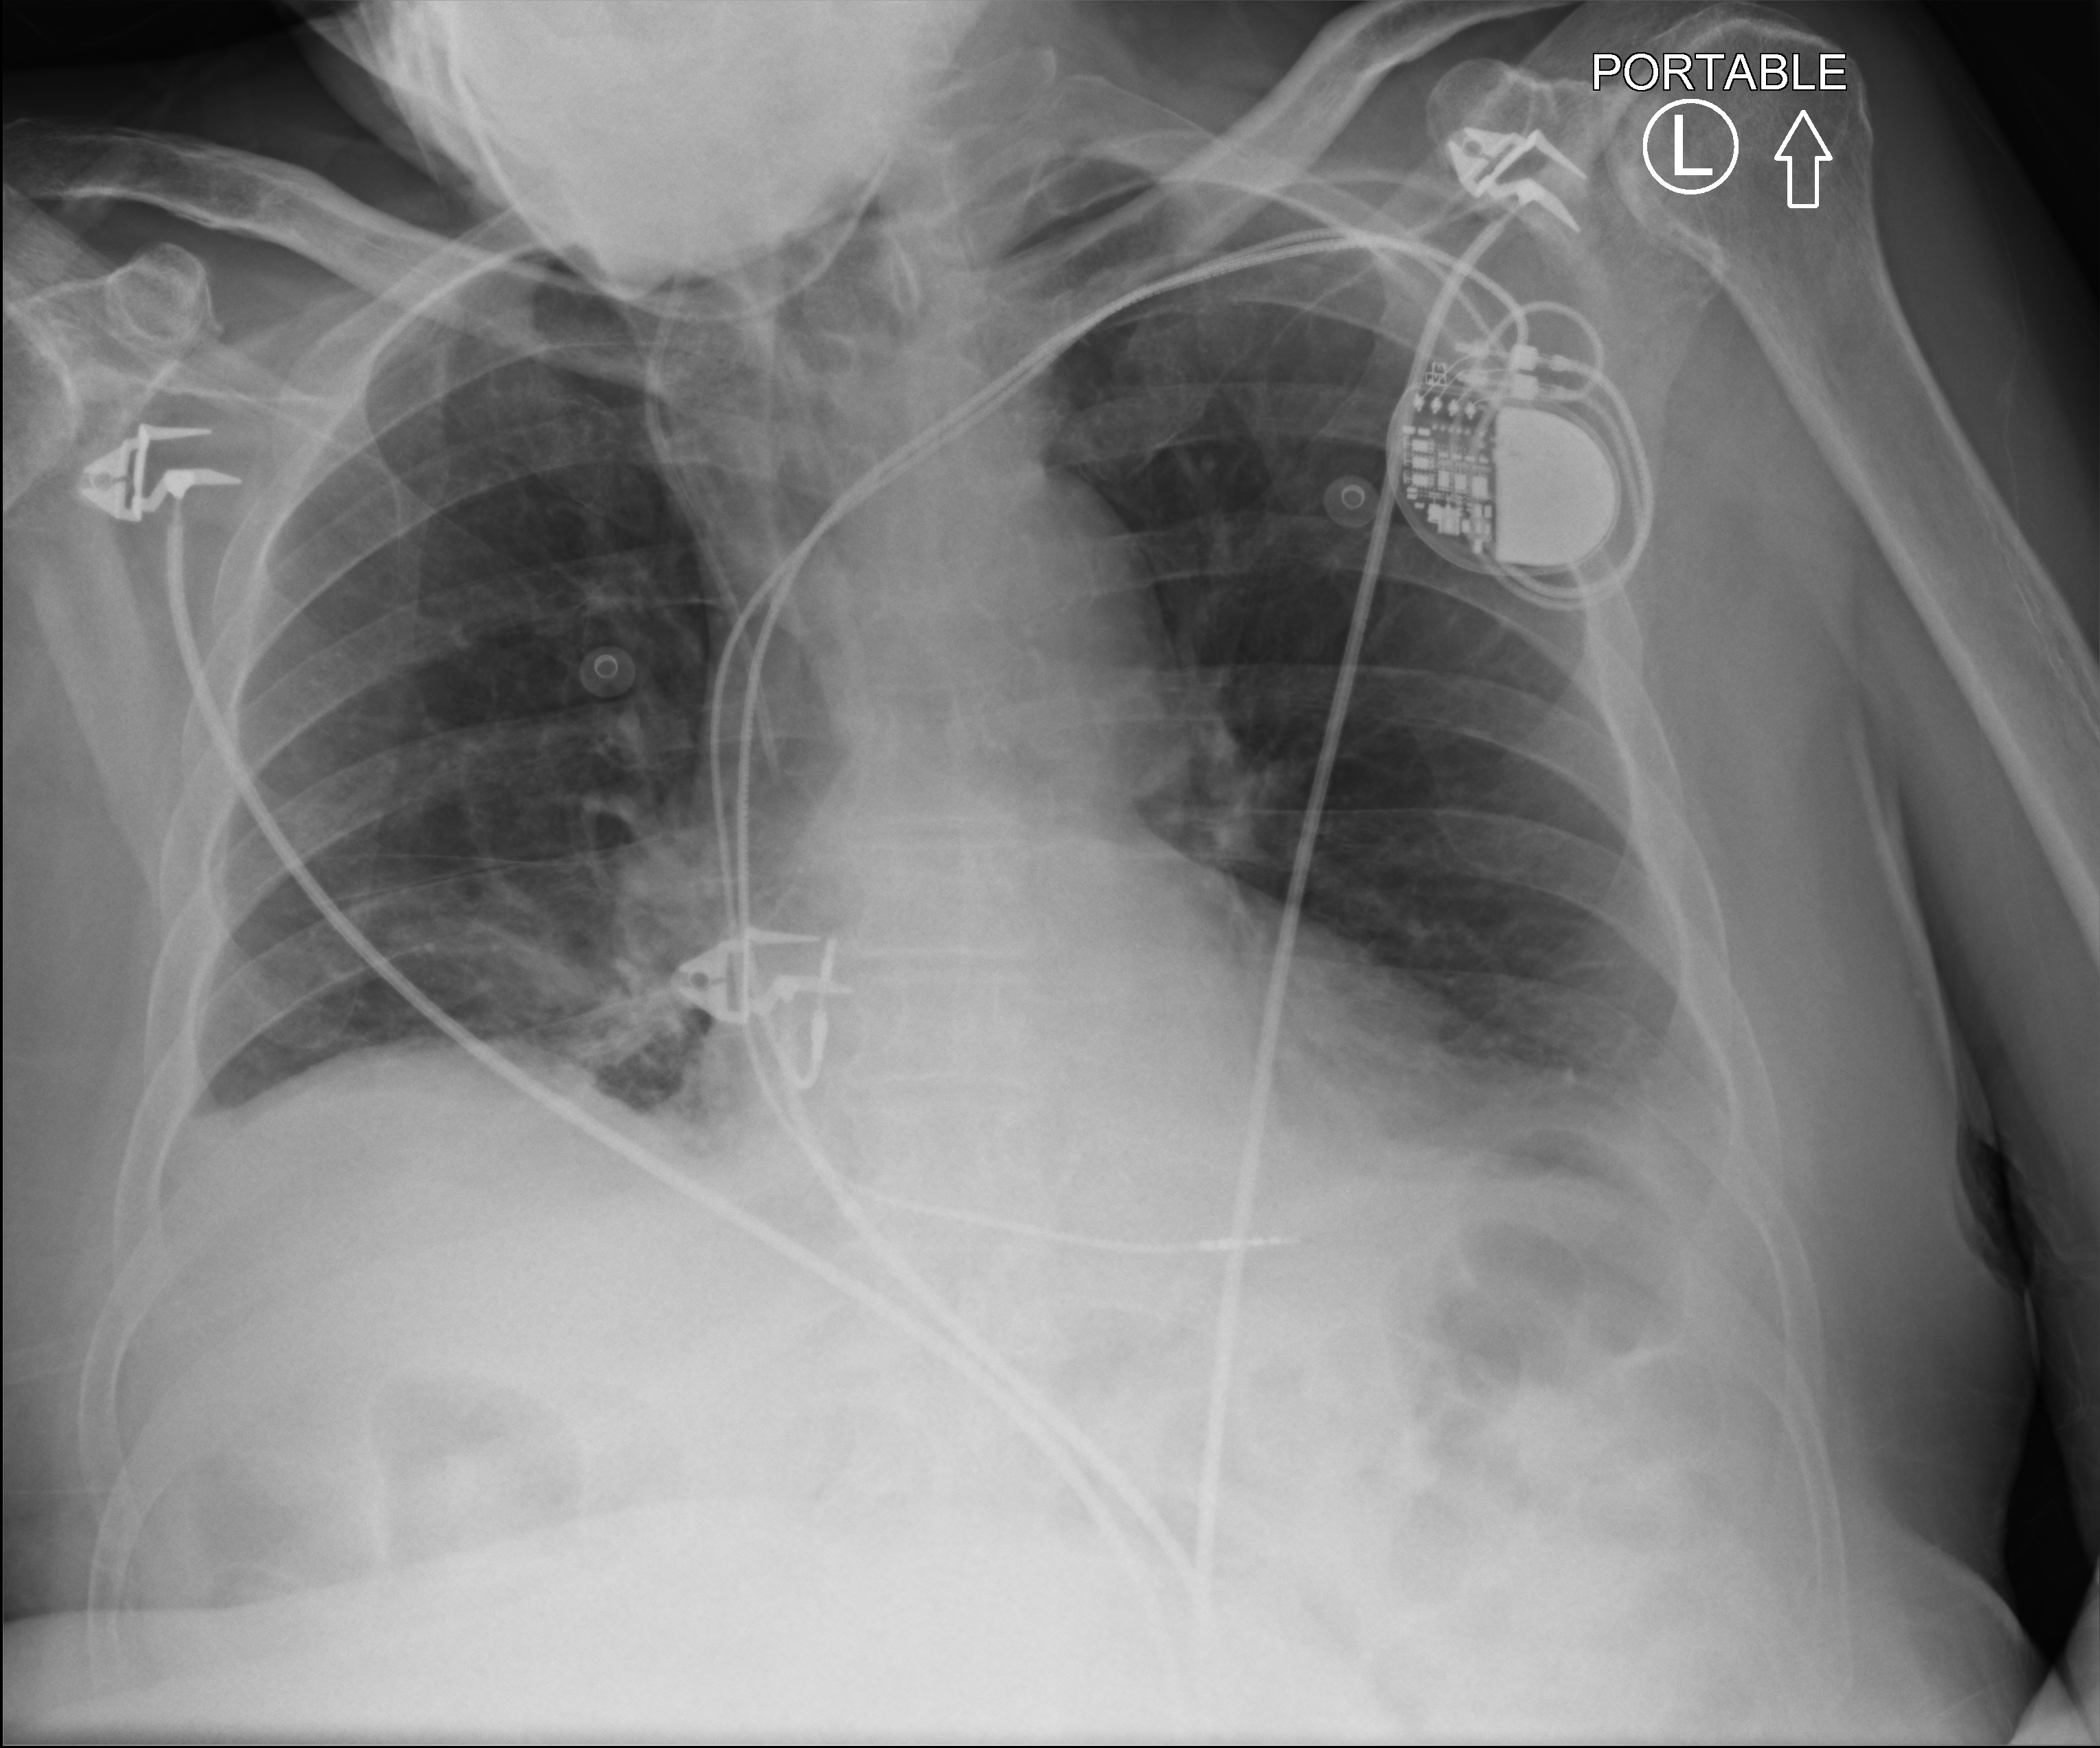
Portable chest radiograph; anteroposterior (AP) projection. Patient hospitalised with COVID-19; male, aged 60–74 years.
Admission-level facts for this patient (not findings on this image; timing relative to this image not recorded):
- other chronic lung disease (admission record): no
- admitted to intensive care during this hospital stay: no